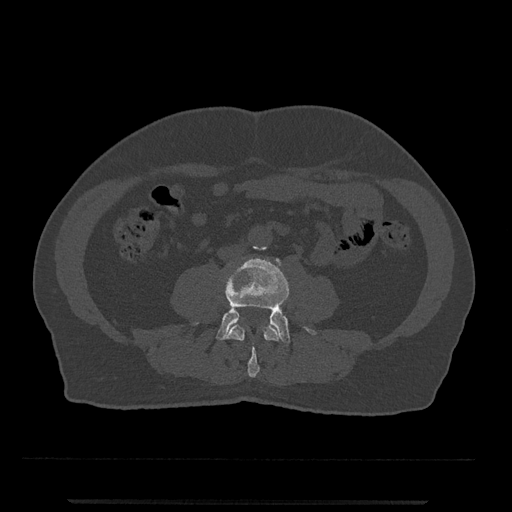
CT including the spine, one axial slice. Position 163 of 797 along the scan axis. 120 kVp. Bone window (W 1800 / L 400 HU). 512 × 512 image matrix. Patient: male, 63 years. From the clinical record (not read from this slice): primary cancer: prostate.
Annotated regions visible in this slice (semi-automatically segmented with operator editing):
- L3 vertebra: bounding box [x1, y1, x2, y2] px = [226, 324, 280, 378]
- L4 vertebra: [196, 258, 317, 344]